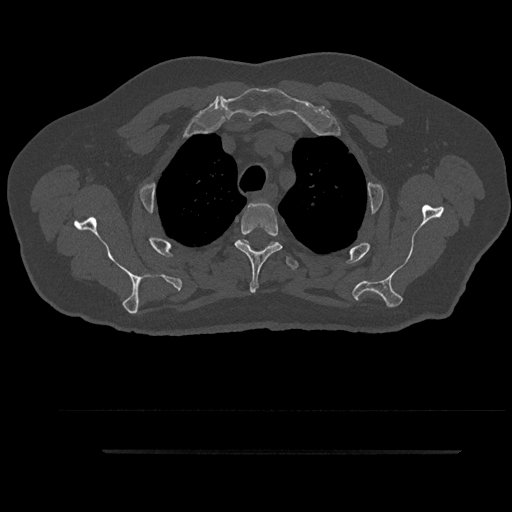
CT including the spine, one axial slice. Slice 711 of 797 in the series (ordered by position). Reconstruction kernel Br40s/3. 120 kVp. Bone window (W 1800 / L 400 HU). 0.5 mm slice thickness. 512 × 512 image matrix, field of view 432 × 432 mm. Male patient, age 63 years. From the clinical record (not read from this slice): primary cancer: renal.
Outlined on this slice (semi-automatic segmentation, software-assisted and operator-edited):
- T3 vertebra: box from (x=235, y=200) to (x=282, y=293) px
- T4 vertebra: (x=244, y=240)–(x=299, y=269)